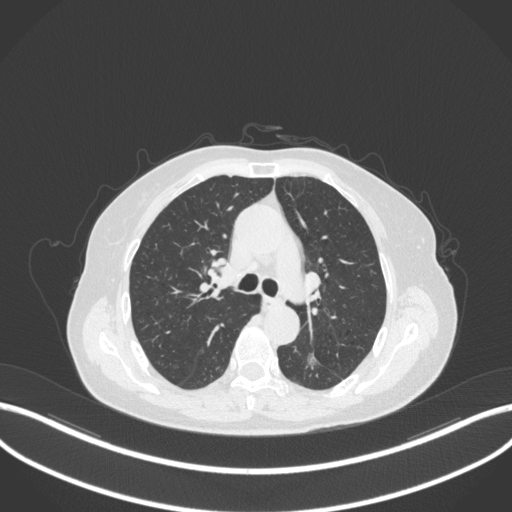
Chest CT, one axial slice; position 198 of 352 along the scan axis; reconstruction kernel B31f; 120 kVp; lung window (W 1500 / L -600 HU); 512 × 512 image matrix, field of view 400 × 400 mm. Patient: female, 70 years. Case-level facts recorded for this patient, not image findings: clinical TNM (as recorded): T1c N0 M0.
Outlined on this slice (rectangle marked by the reading radiologist):
- lung tumour (recorded histology: adenocarcinoma): box from (x=300, y=346) to (x=323, y=374) px